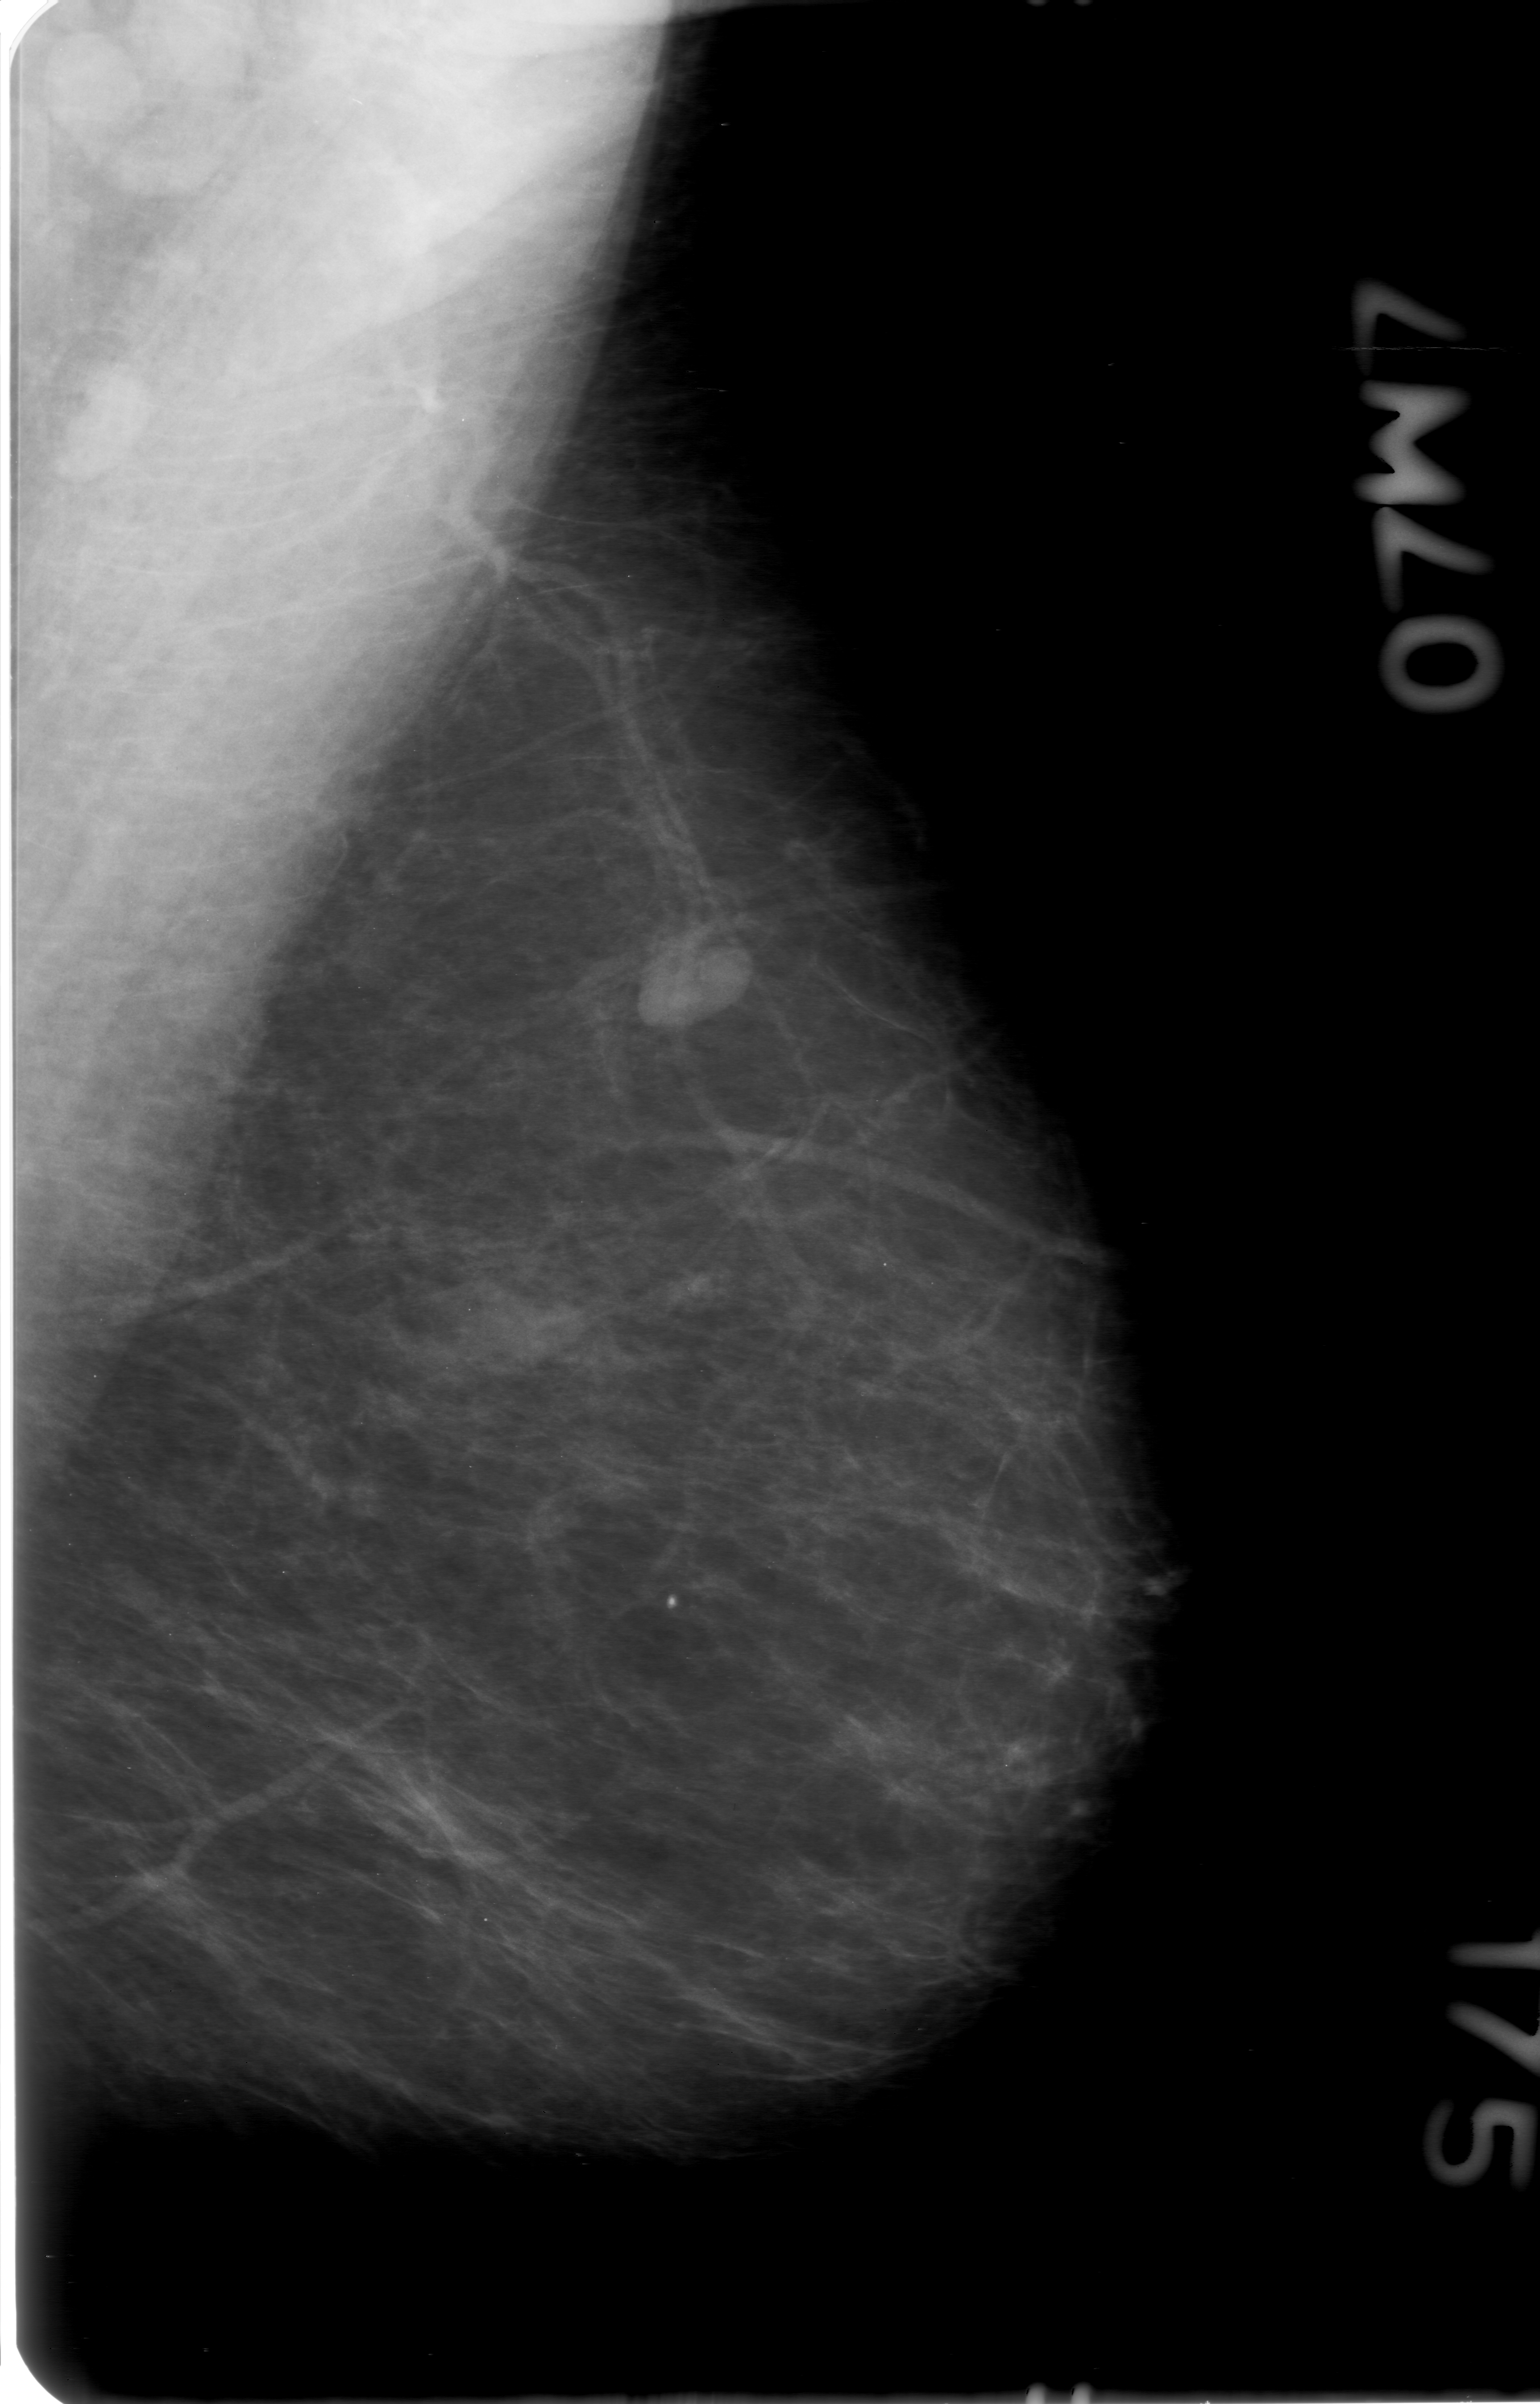
Digitized screen-film mammogram; left breast; MLO view; BI-RADS breast density category 1 (scale 1–4).
Marked abnormality: mass, shape lobulated, margins obscured; BI-RADS assessment category 0 (incomplete: needs additional imaging); subtlety rating 4 on a 1 (subtle) to 5 (obvious) scale; pathology result (as recorded, not read from the image): benign.